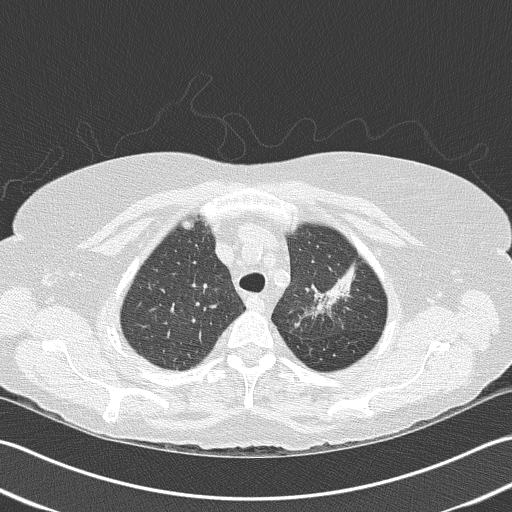
Low-dose screening chest CT, axial slice. Baseline annual screen. Lung window (W 1500 / L -600 HU). 2 mm slice thickness. Female participant, aged 68 years at enrolment.
Expert reader's lesion annotation, box from (x=293, y=248) to (x=367, y=324) px. Screening reader's record for this exam: no non-calcified nodule ≥4 mm recorded.